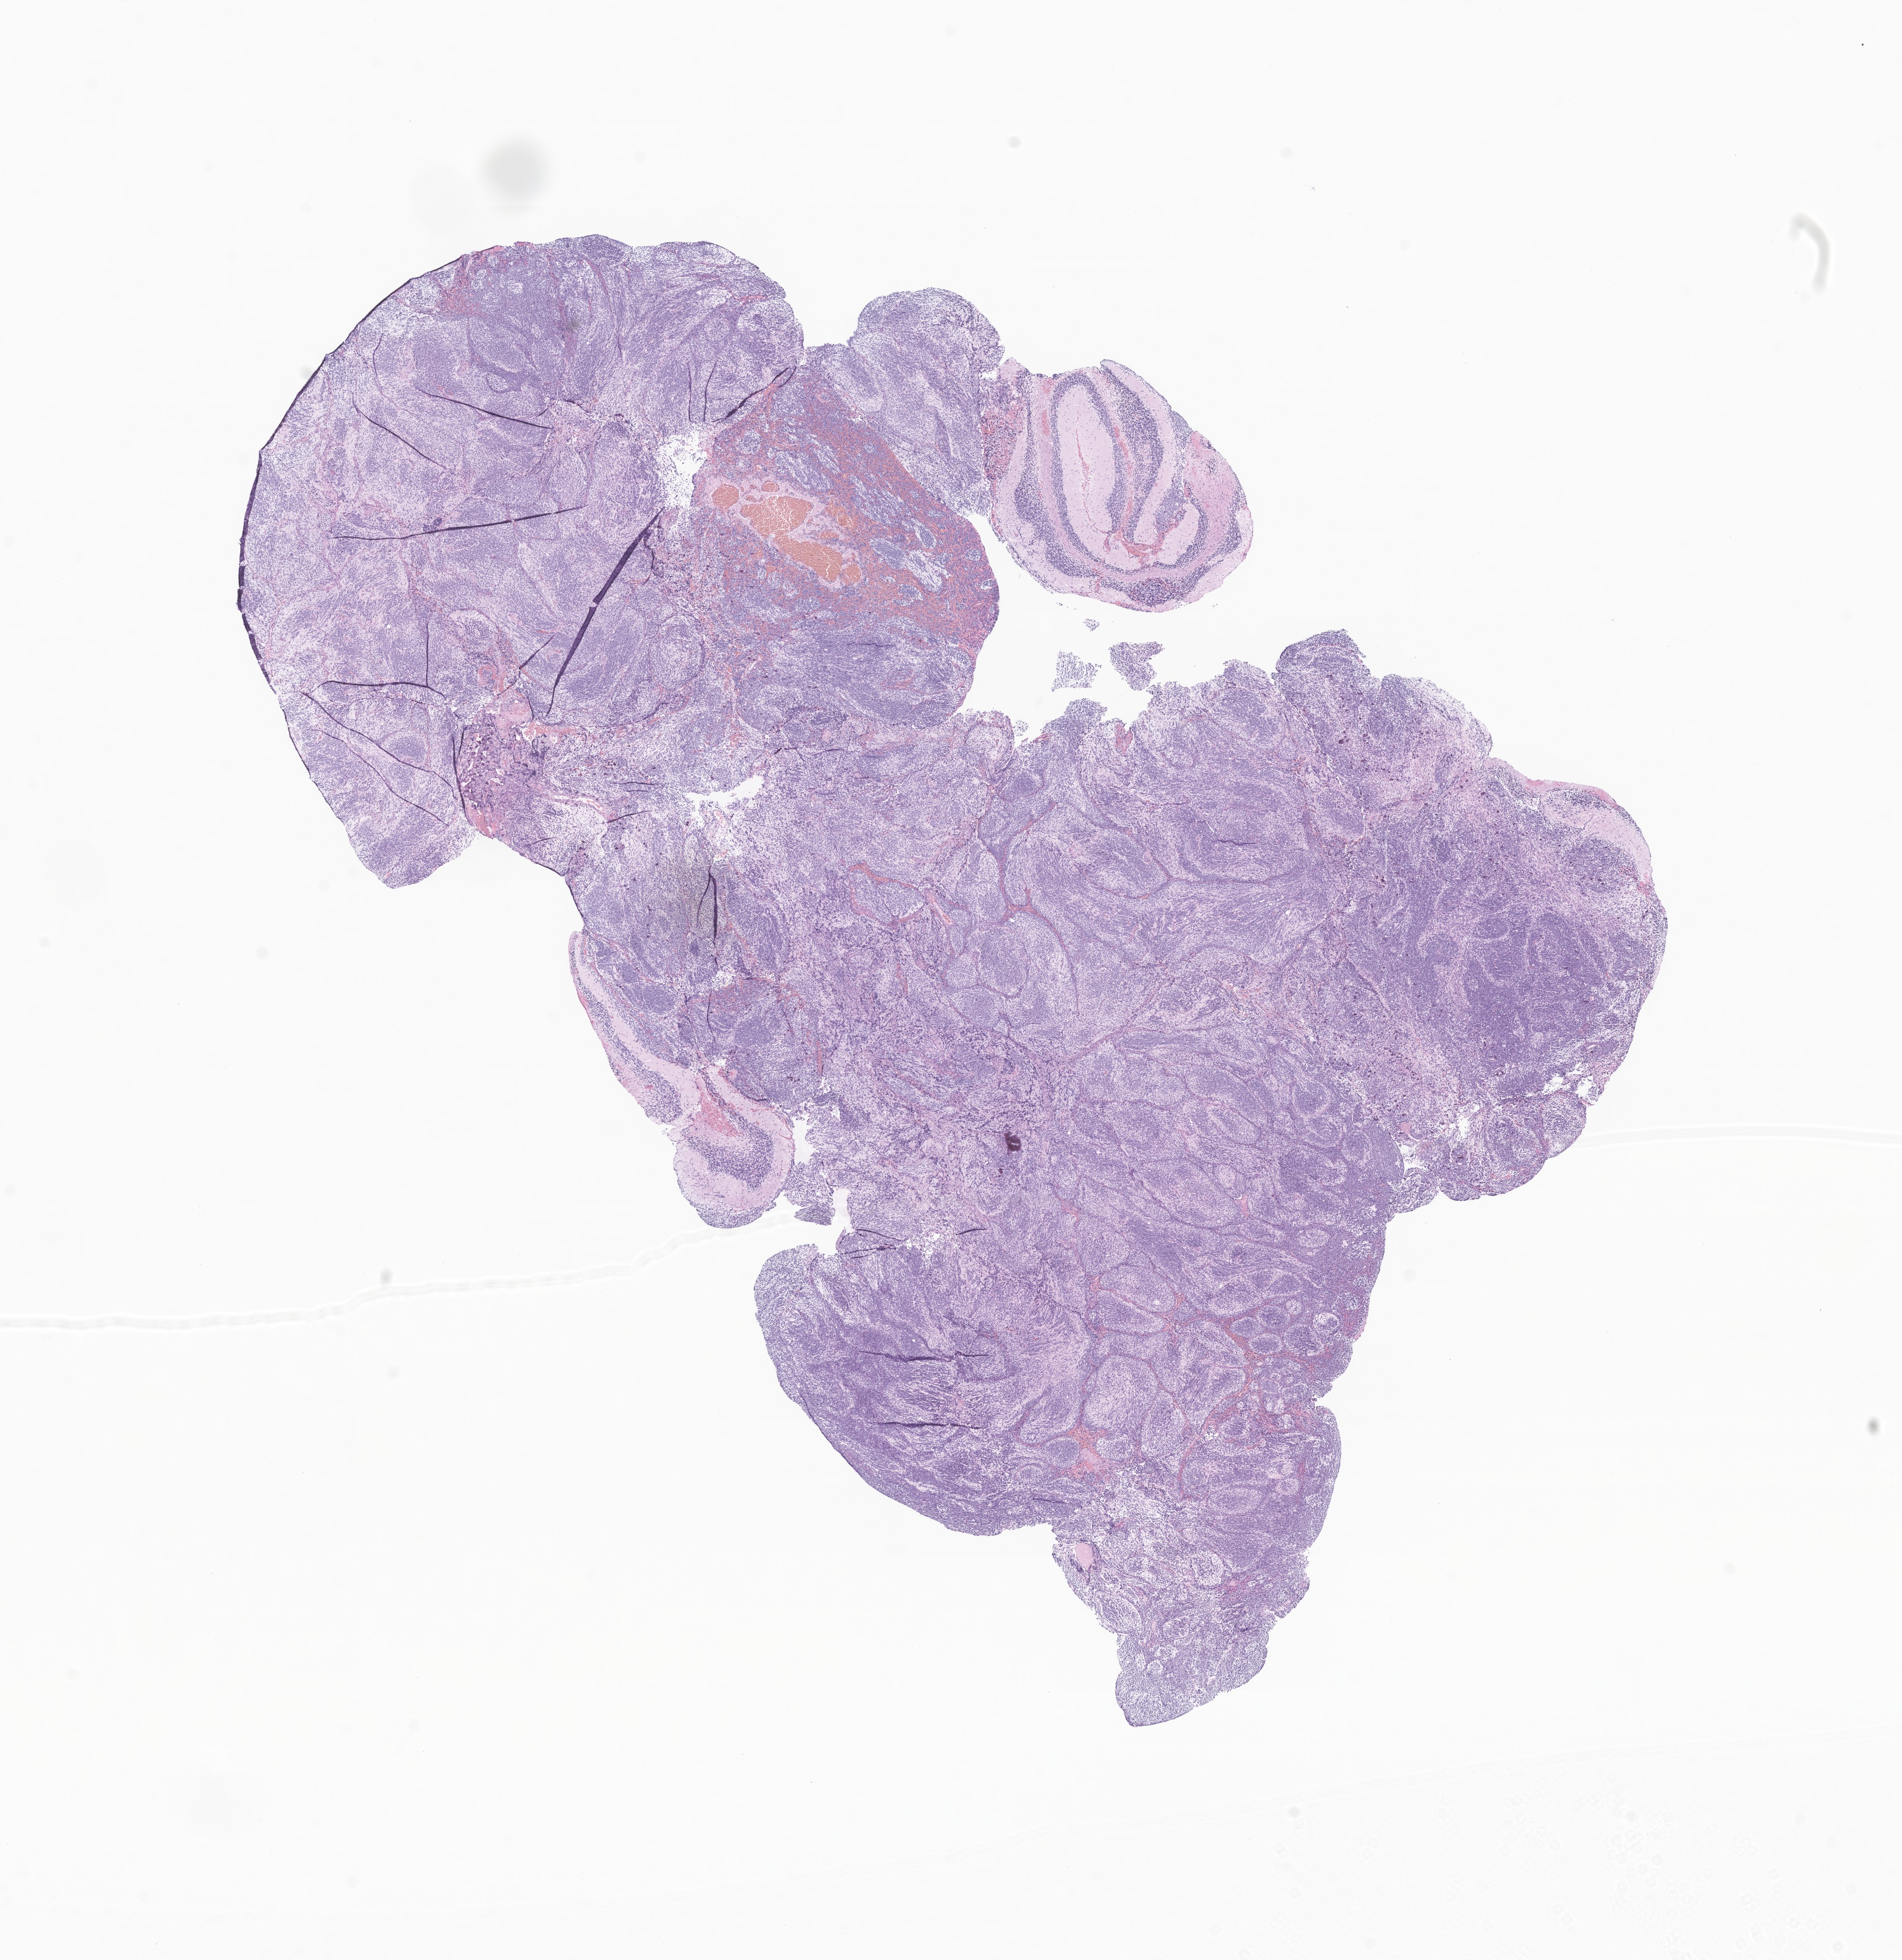
Whole-slide image, haematoxylin and eosin stain of tumor tissue from the cerebellum, whole scanned area (about 15.1 x 15.5 mm) shown as a low-resolution overview; formalin-fixed, paraffin-embedded (FFPE) tissue. Male patient, age 320 days.
Recorded diagnosis: Medulloblastoma, NOS.